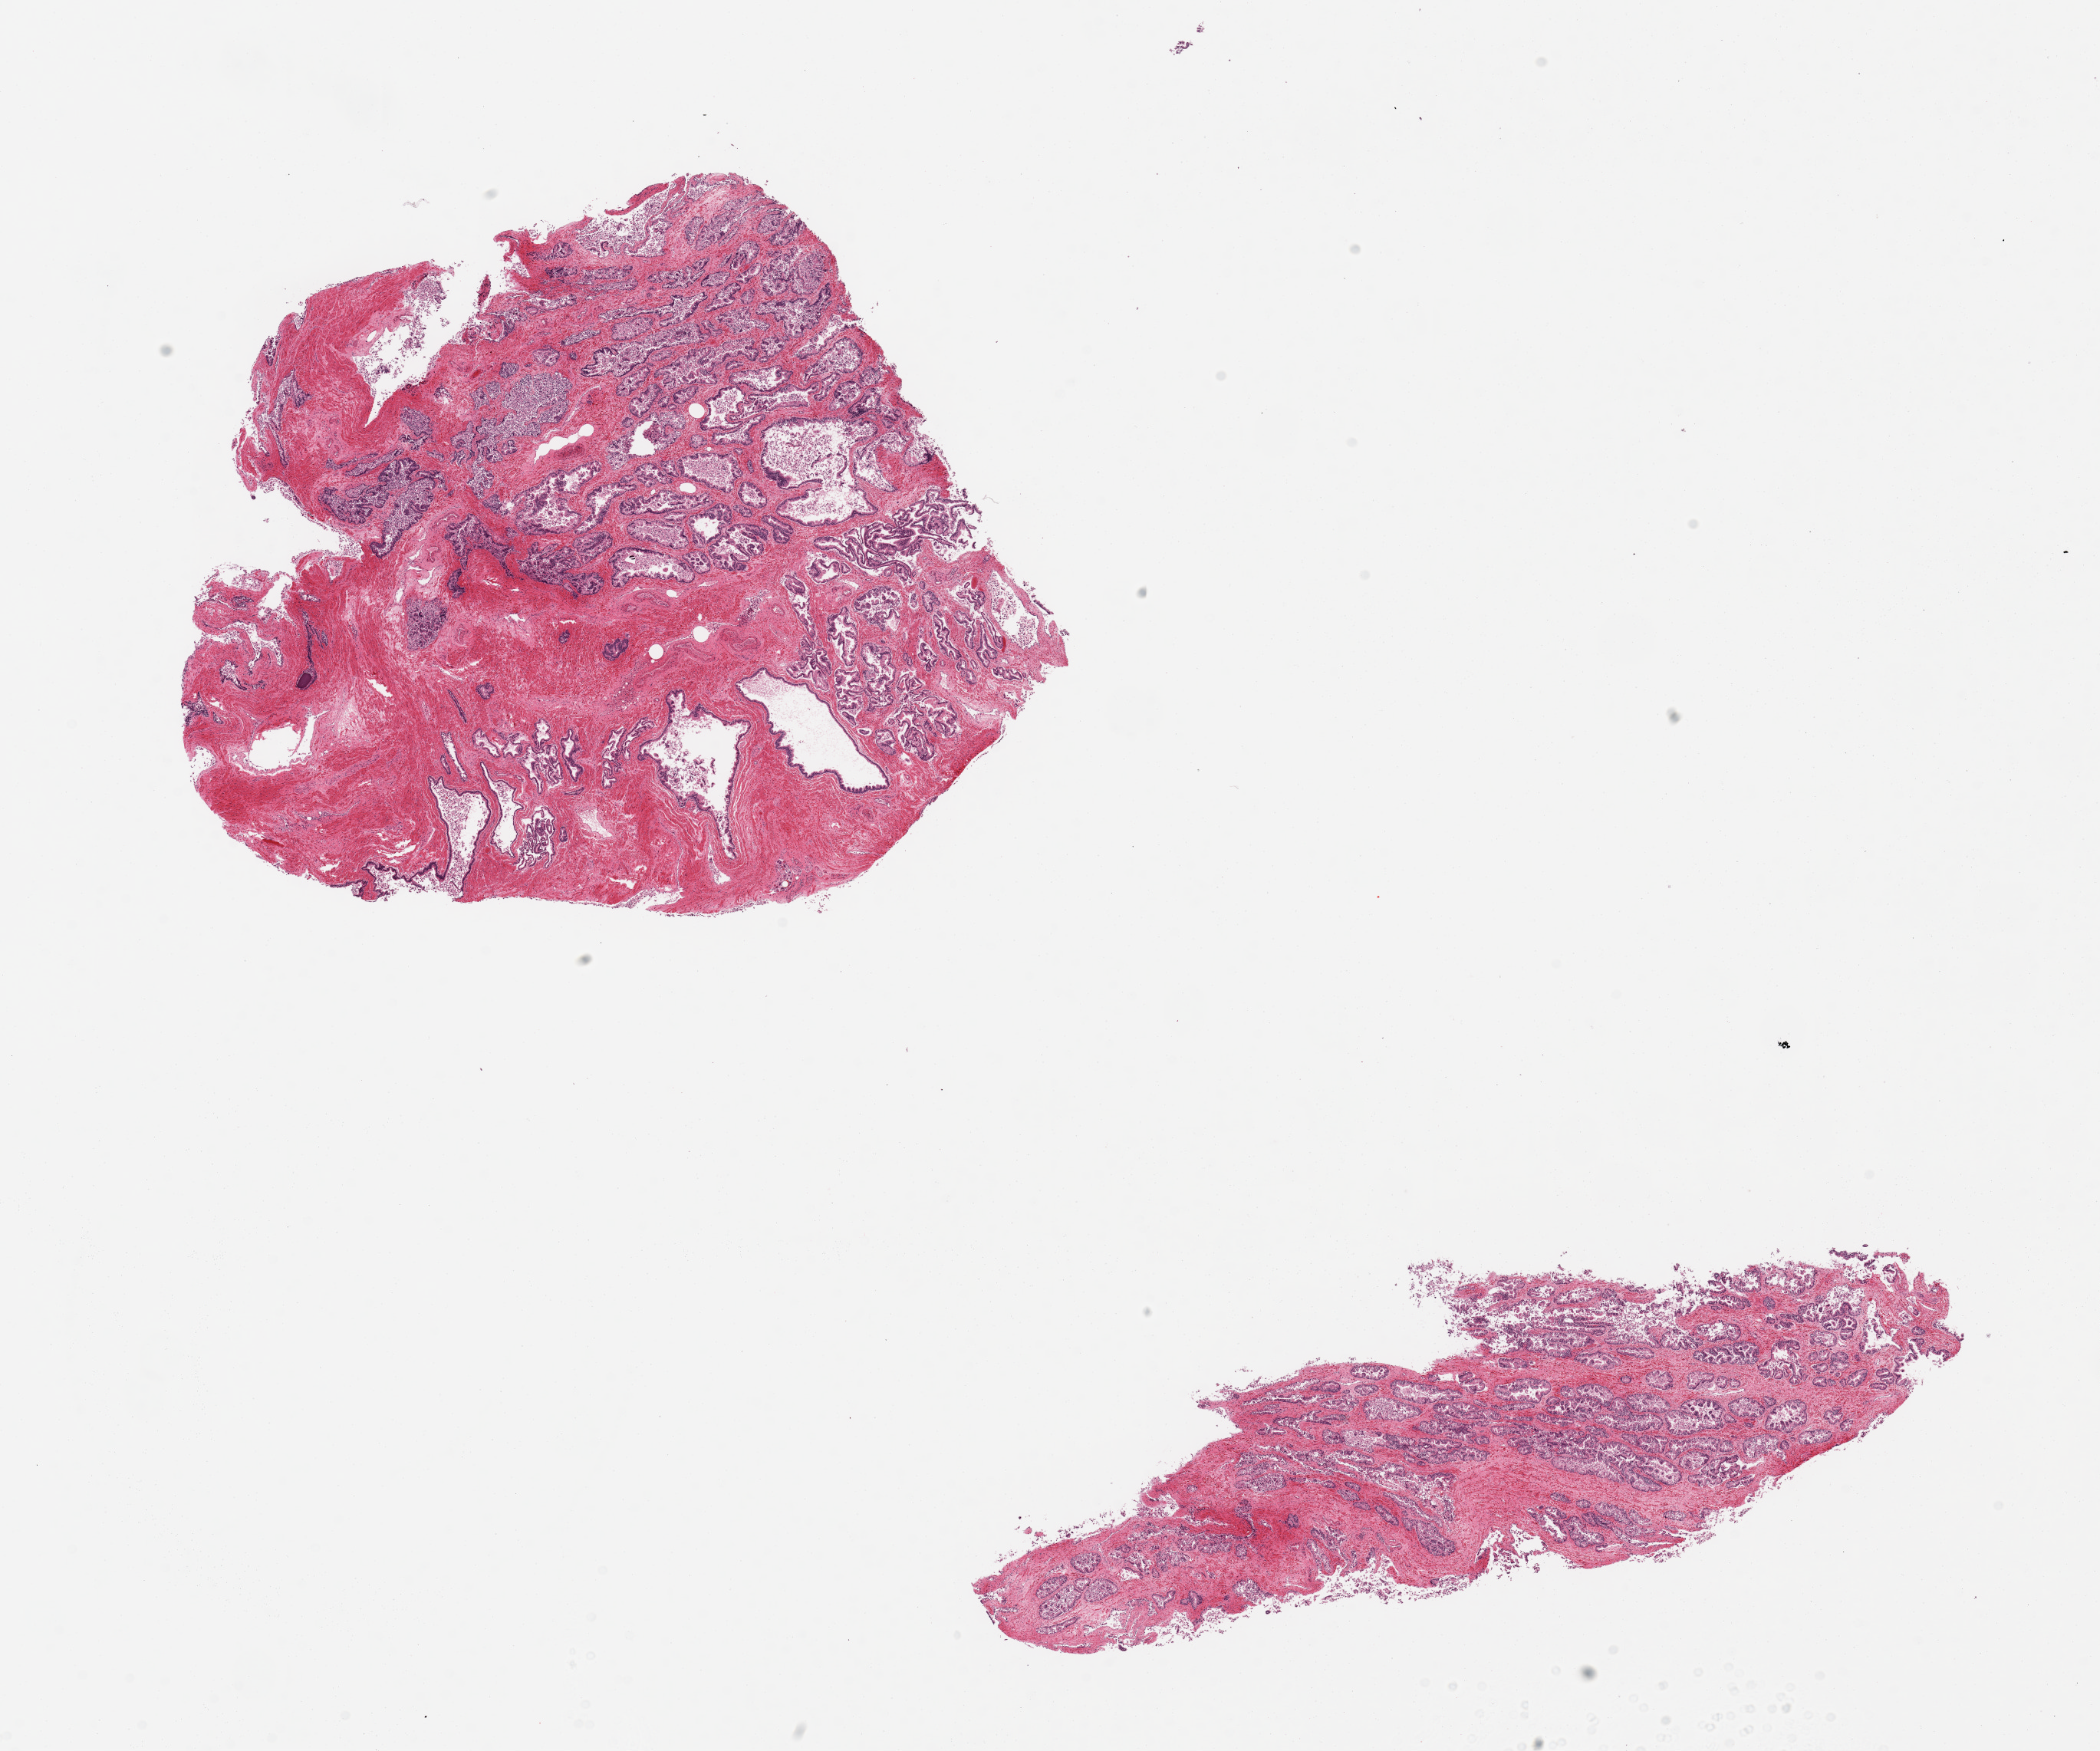
Hematoxylin and eosin (H&E) whole-slide image — shown as a low-resolution overview of the whole scanned area (about 21.7 x 18.1 mm, slide scanned at 20x), PAXgene-fixed paraffin-embedded (PFPE) section, target tissue: prostate, tissue donor sample.
* review note (as recorded): 2 pieces, mild glandular hyperplasia. Glandular elements beginning to slough into lumina